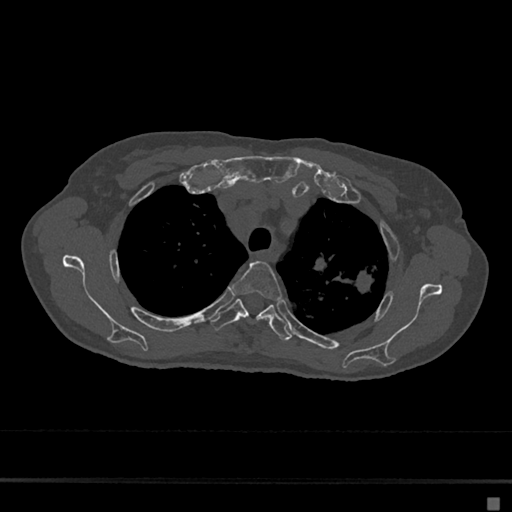
CT including the spine, one axial slice. Position 521 of 797 along the scan axis. Bone window (W 1800 / L 400 HU). 0.5 mm slice thickness. 512 × 512 image matrix, field of view 360 × 360 mm. Patient: female, 68 years. Case-level facts recorded for this patient, not image findings: primary cancer: renal.
Annotated regions visible in this slice (semi-automatic segmentation, software-assisted and operator-edited):
- T3 vertebra: bounding box (x1, y1, x2, y2) in pixels: (231, 261, 282, 318)
- T4 vertebra: (210, 299, 291, 341)